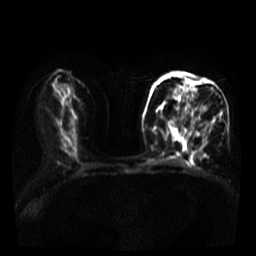
Breast MRI, one axial slice. Slice 15 of 39 in the series (ordered by position). Diffusion-weighted series; image 2 of 4 stored at this slice position (different b-values; order by instance number). 3 T. 5 mm slice thickness. 256 × 256 image matrix, field of view 320 × 320 mm. Female patient.
Outlined on this slice (outlined manually by an expert reader):
- tumour on diffusion-weighted imaging: bounding box <157,86,205,120> (left, top, right, bottom; pixels)